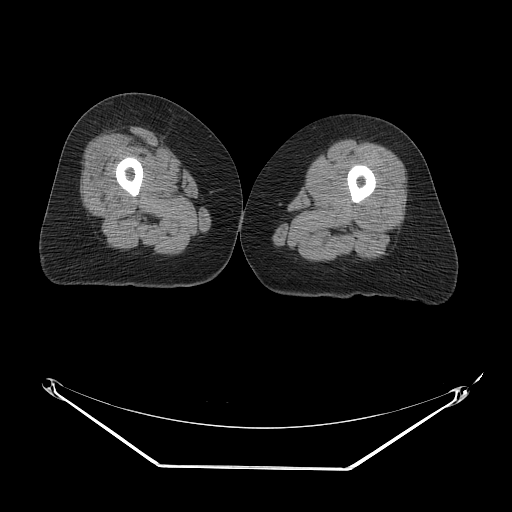
CT of an extremity soft-tissue mass (from a PET/CT study), one axial slice; slice 14 of 267 in the series (ordered by position); reconstruction kernel STANDARD; 140 kVp; soft-tissue window (W 400 / L 40 HU); 512 × 512 image matrix. Female patient. From the clinical record (not read from this slice): histological type: malignant solitary fibrous tumor; grade: intermediate; site of the primary tumour: right thigh.
Annotated regions visible in this slice (expert contour drawn on MRI and transferred to this co-registered scan by the dataset authors):
- gross tumour volume including surrounding oedema: bounding box (x1, y1, x2, y2) in pixels: (128, 130, 181, 165)